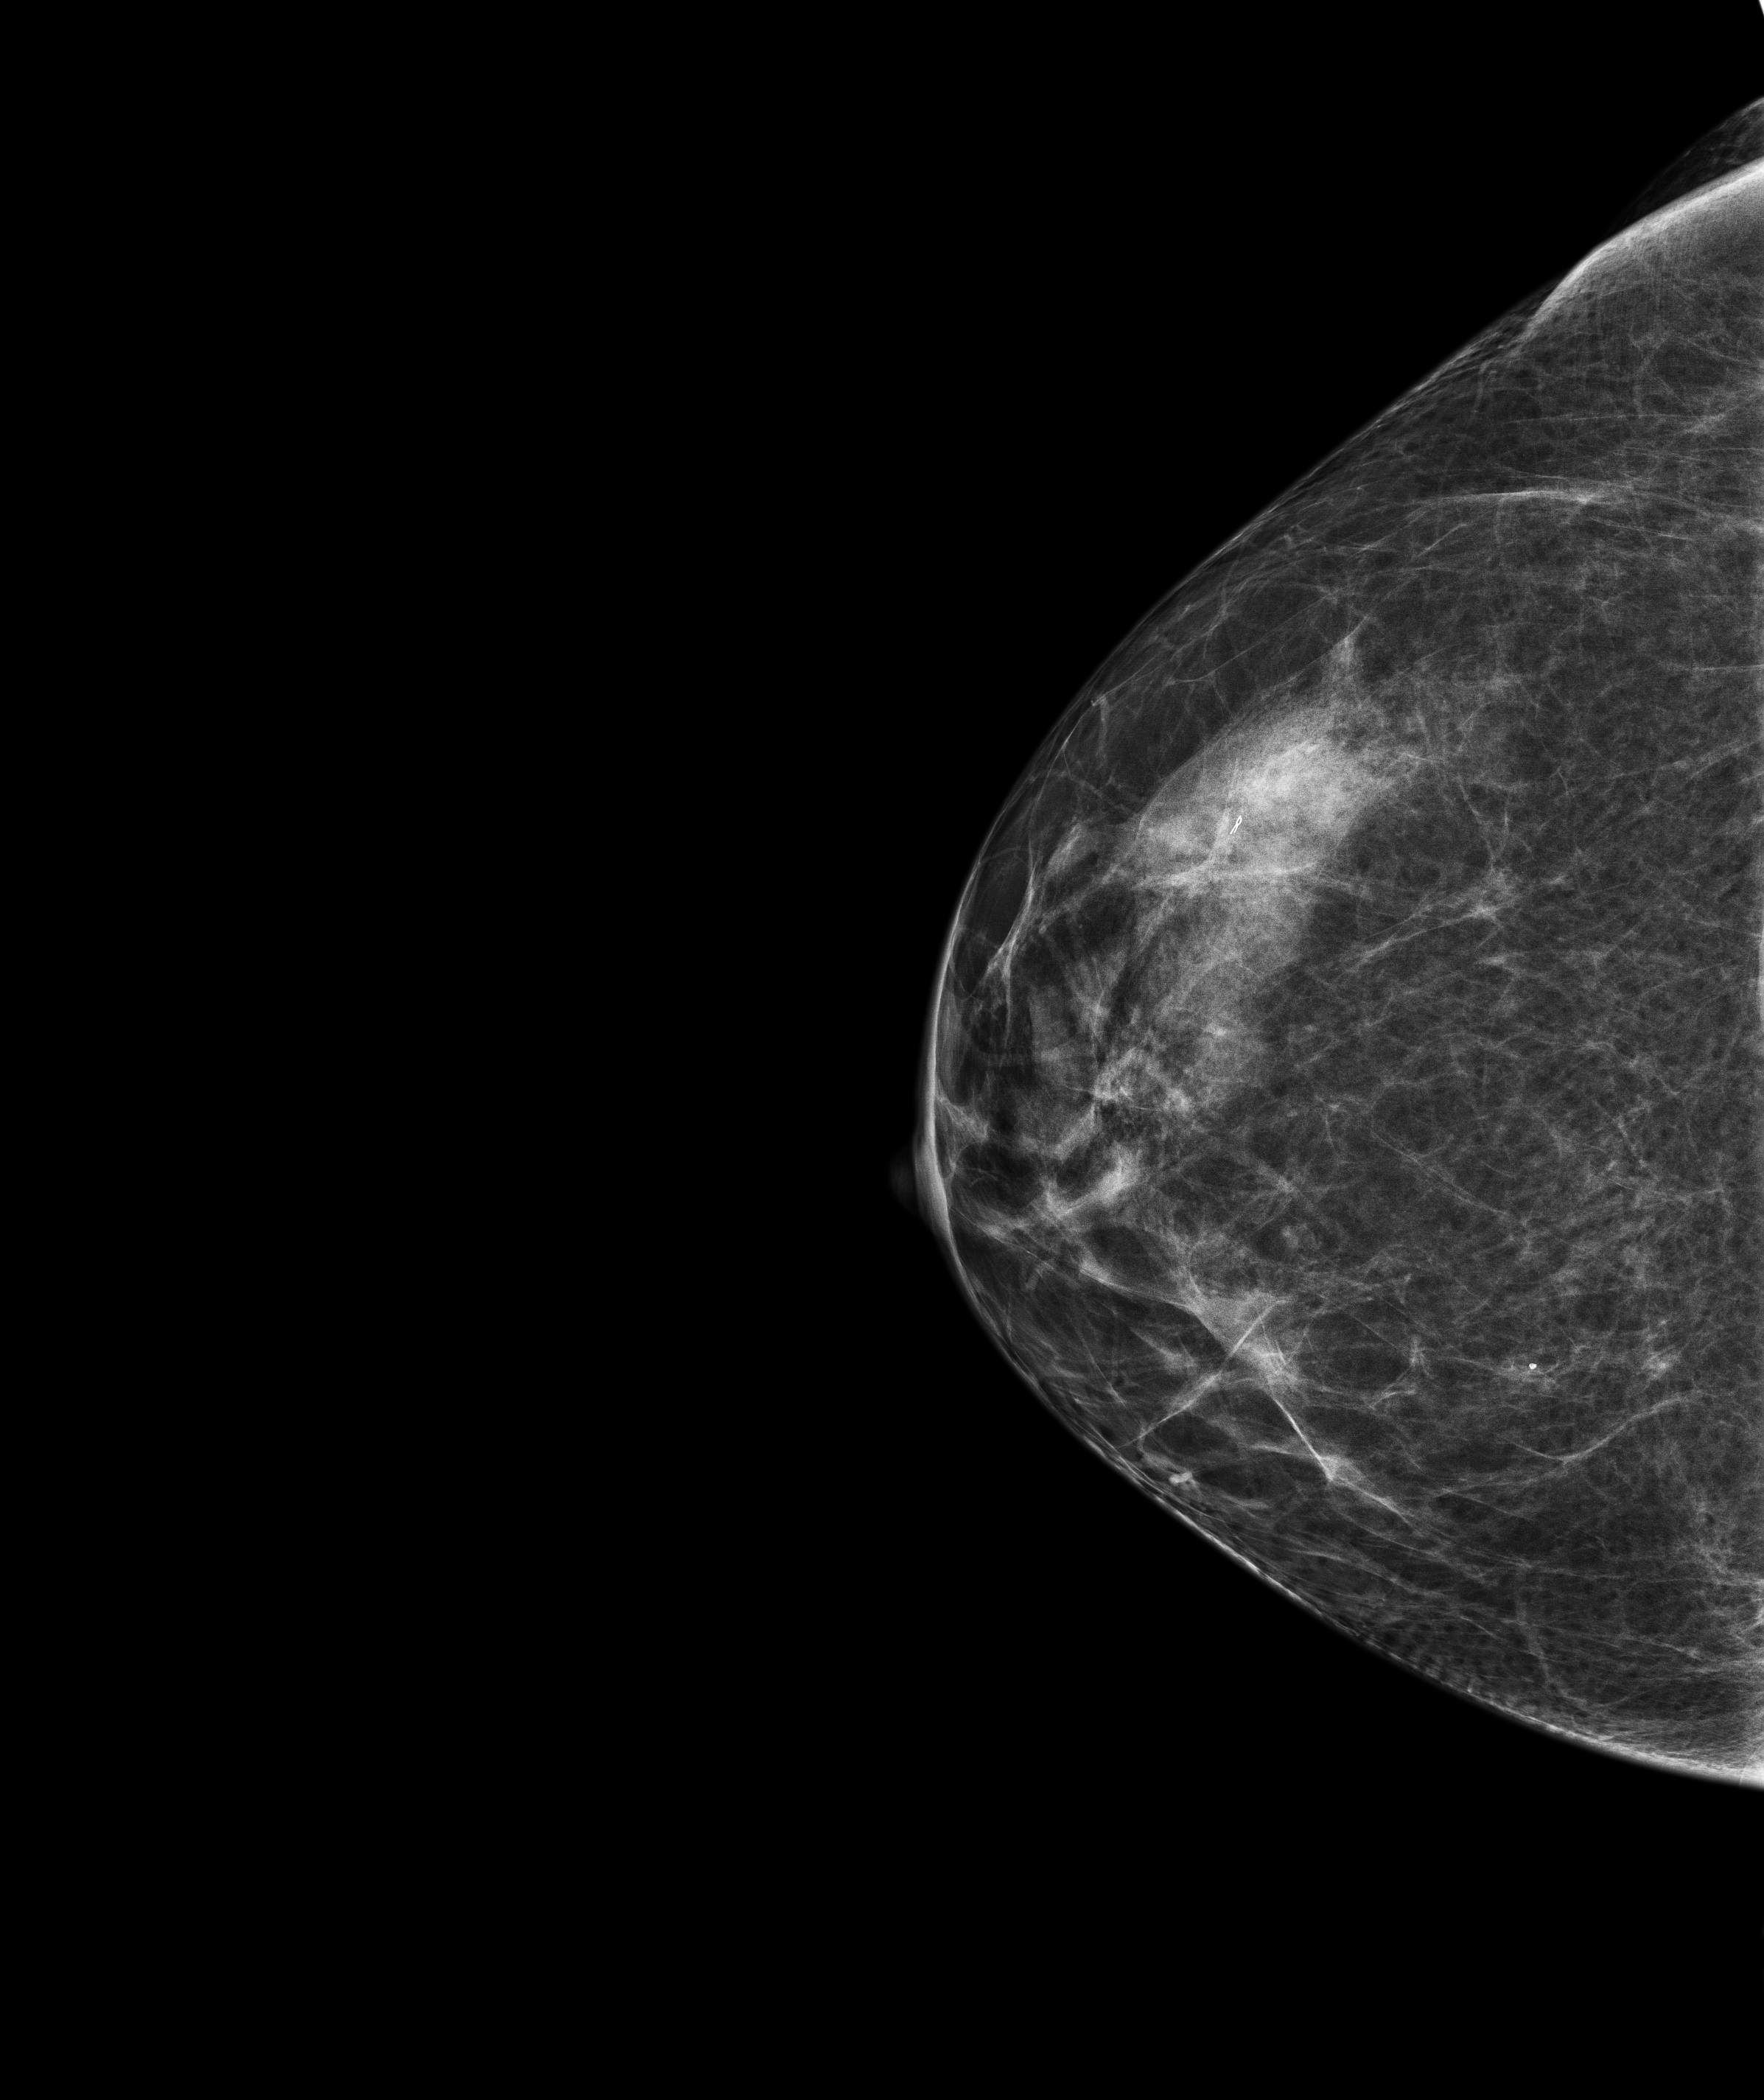
Screening examination, system: Senographe Pristina. Patient: female, 49 years.
Image type: full-field digital mammogram. Breast: right. Projection: cranio-caudal projection.